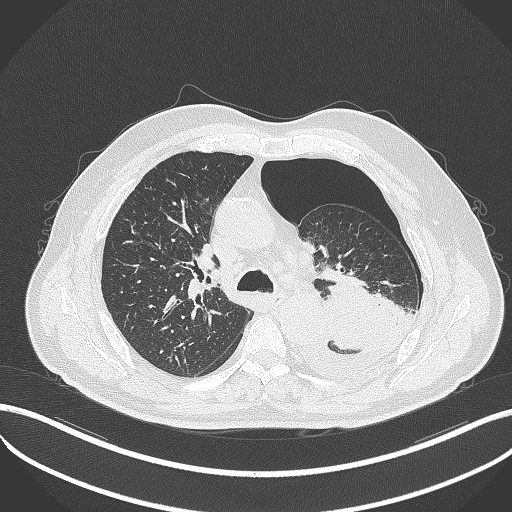
Chest CT, one axial slice. Position 343 of 464 along the scan axis. Reconstruction kernel B70f. Lung window (W 1500 / L -600 HU). 1 mm slice thickness. 512 × 512 image matrix, field of view 400 × 400 mm. Male patient, age 76 years. From the clinical record (not read from this slice): clinical TNM (as recorded): T3 N0 M1b.
Outlined on this slice (rectangle marked by the reading radiologist):
- lung tumour (recorded histology: adenocarcinoma): bounding box <317,270,405,352> (left, top, right, bottom; pixels)